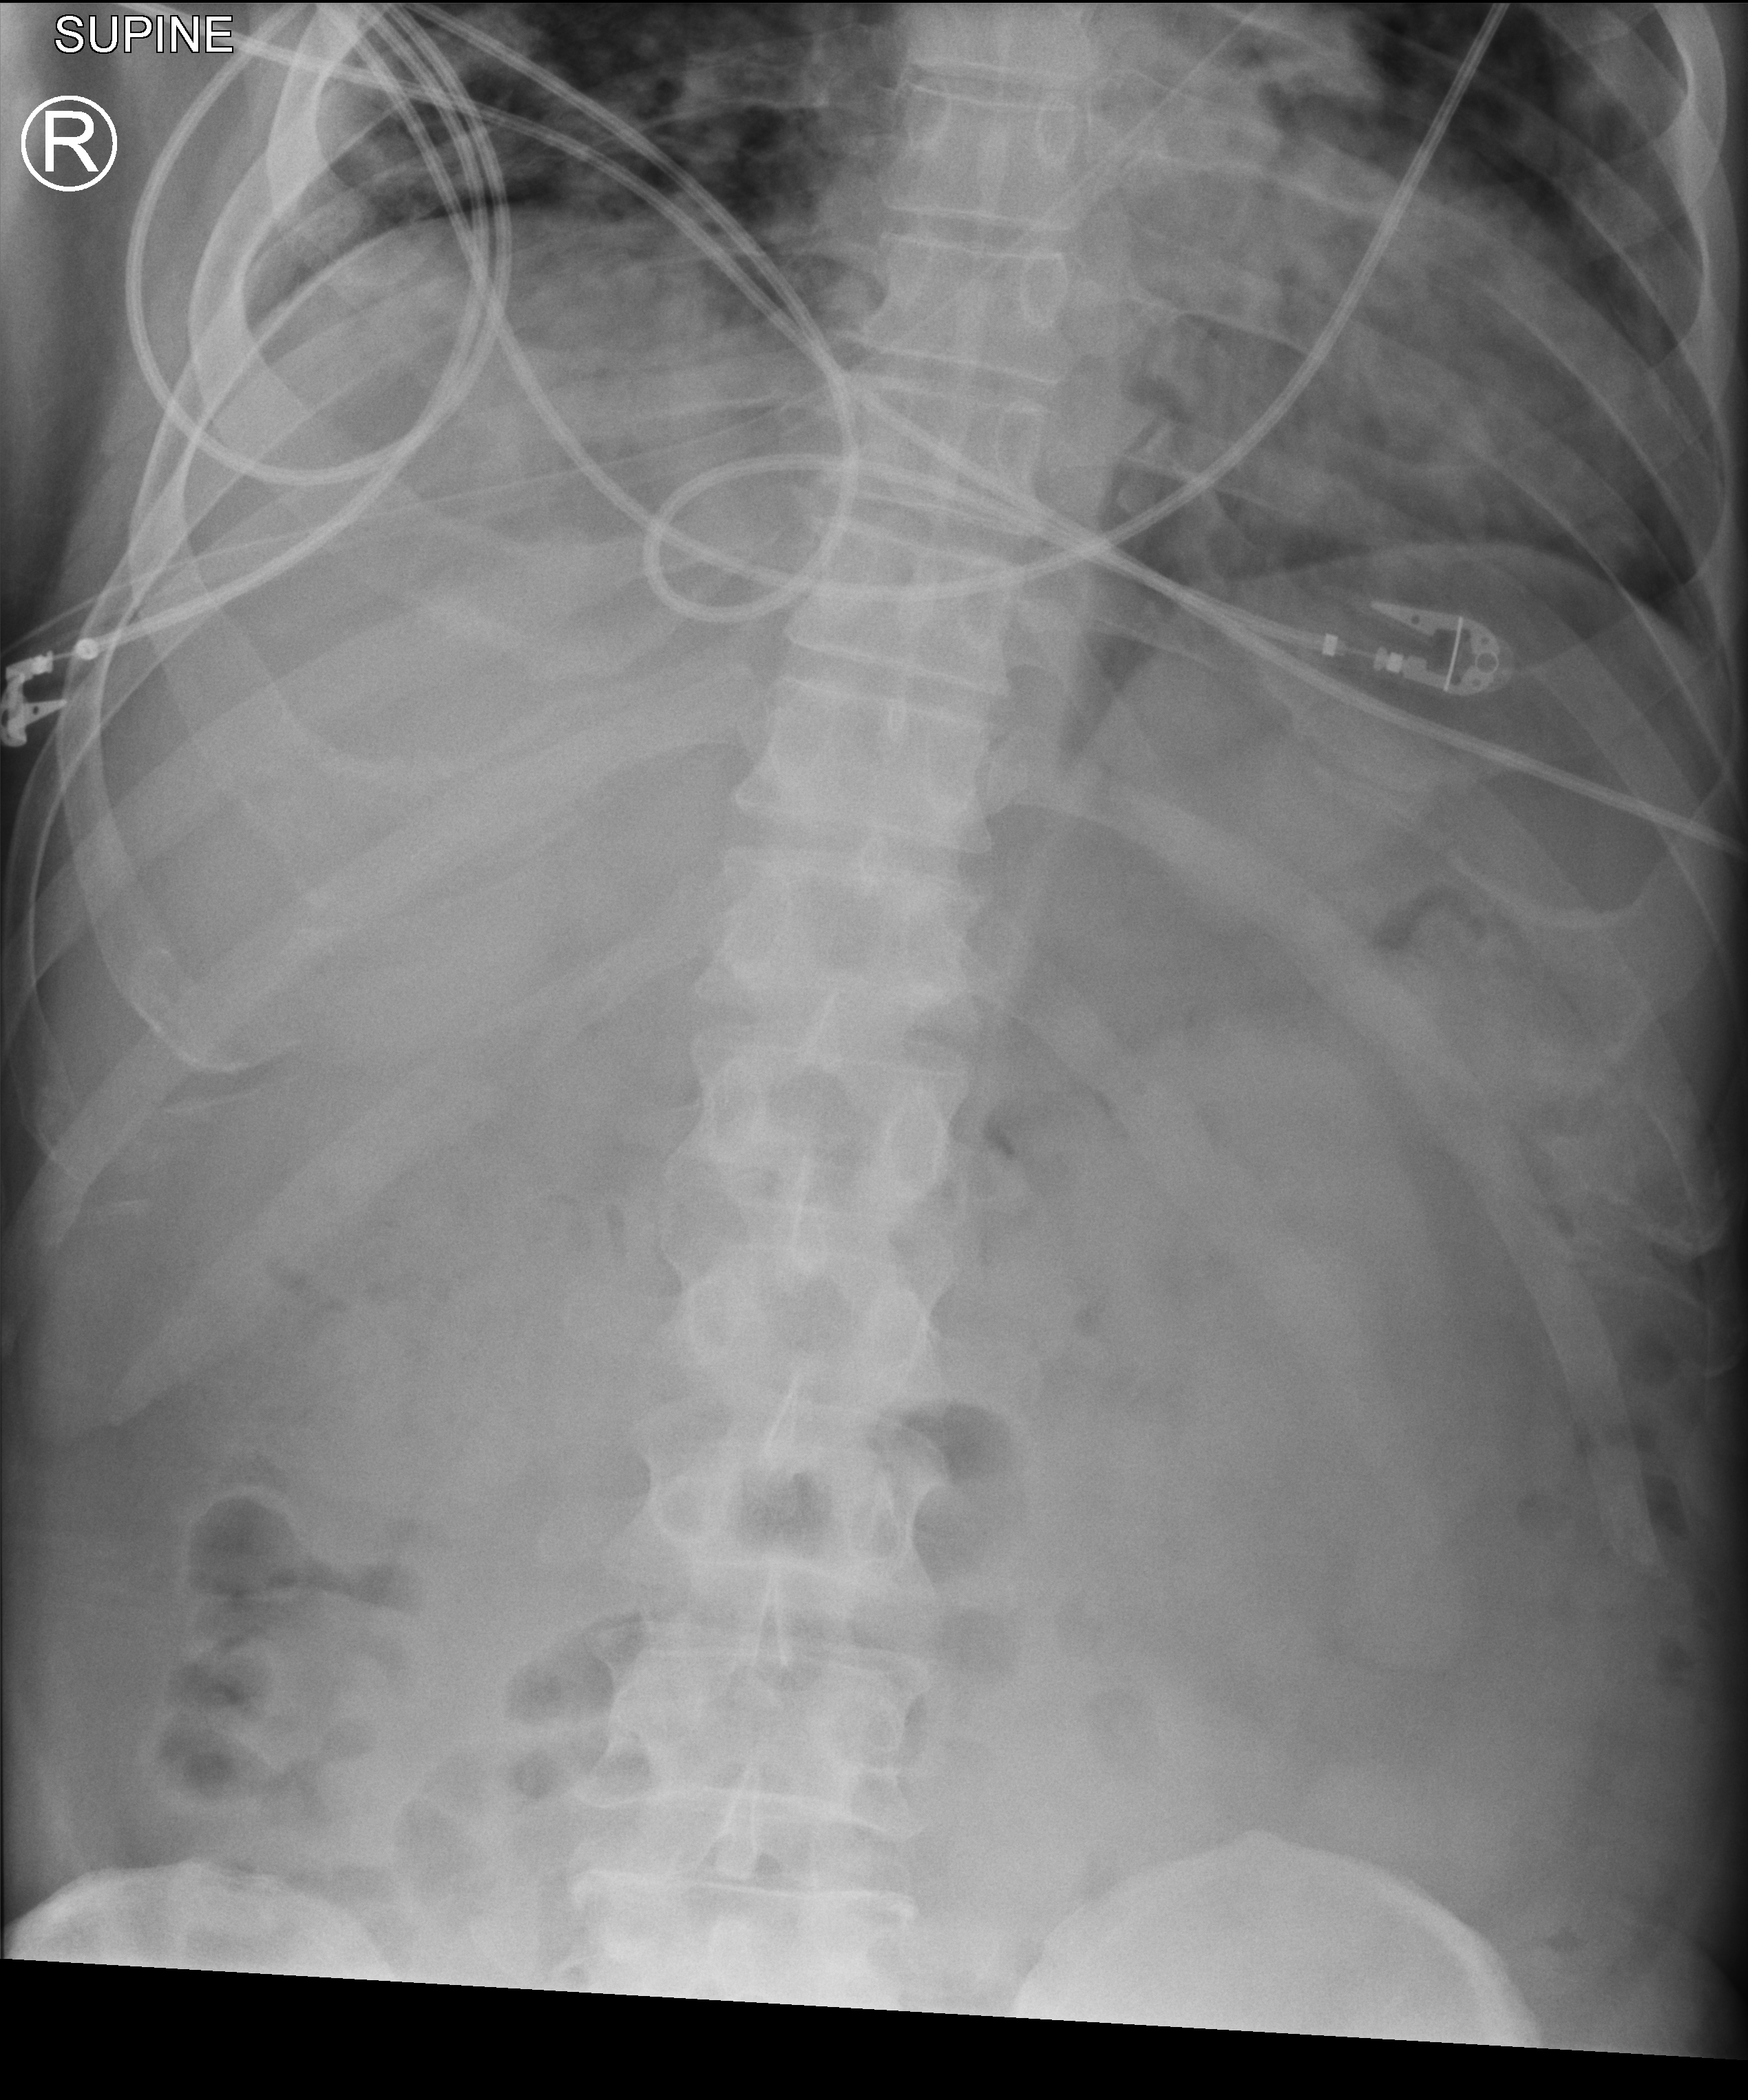
Portable abdomen radiograph, anteroposterior (AP) projection. Male patient hospitalised with COVID-19, age 18–59 years.
From the hospital-stay record, not from the radiograph (when in the stay this image was taken is not recorded): mechanically ventilated during this hospital stay: yes; length of hospital stay: 32 days; admitted to intensive care during this hospital stay: no.